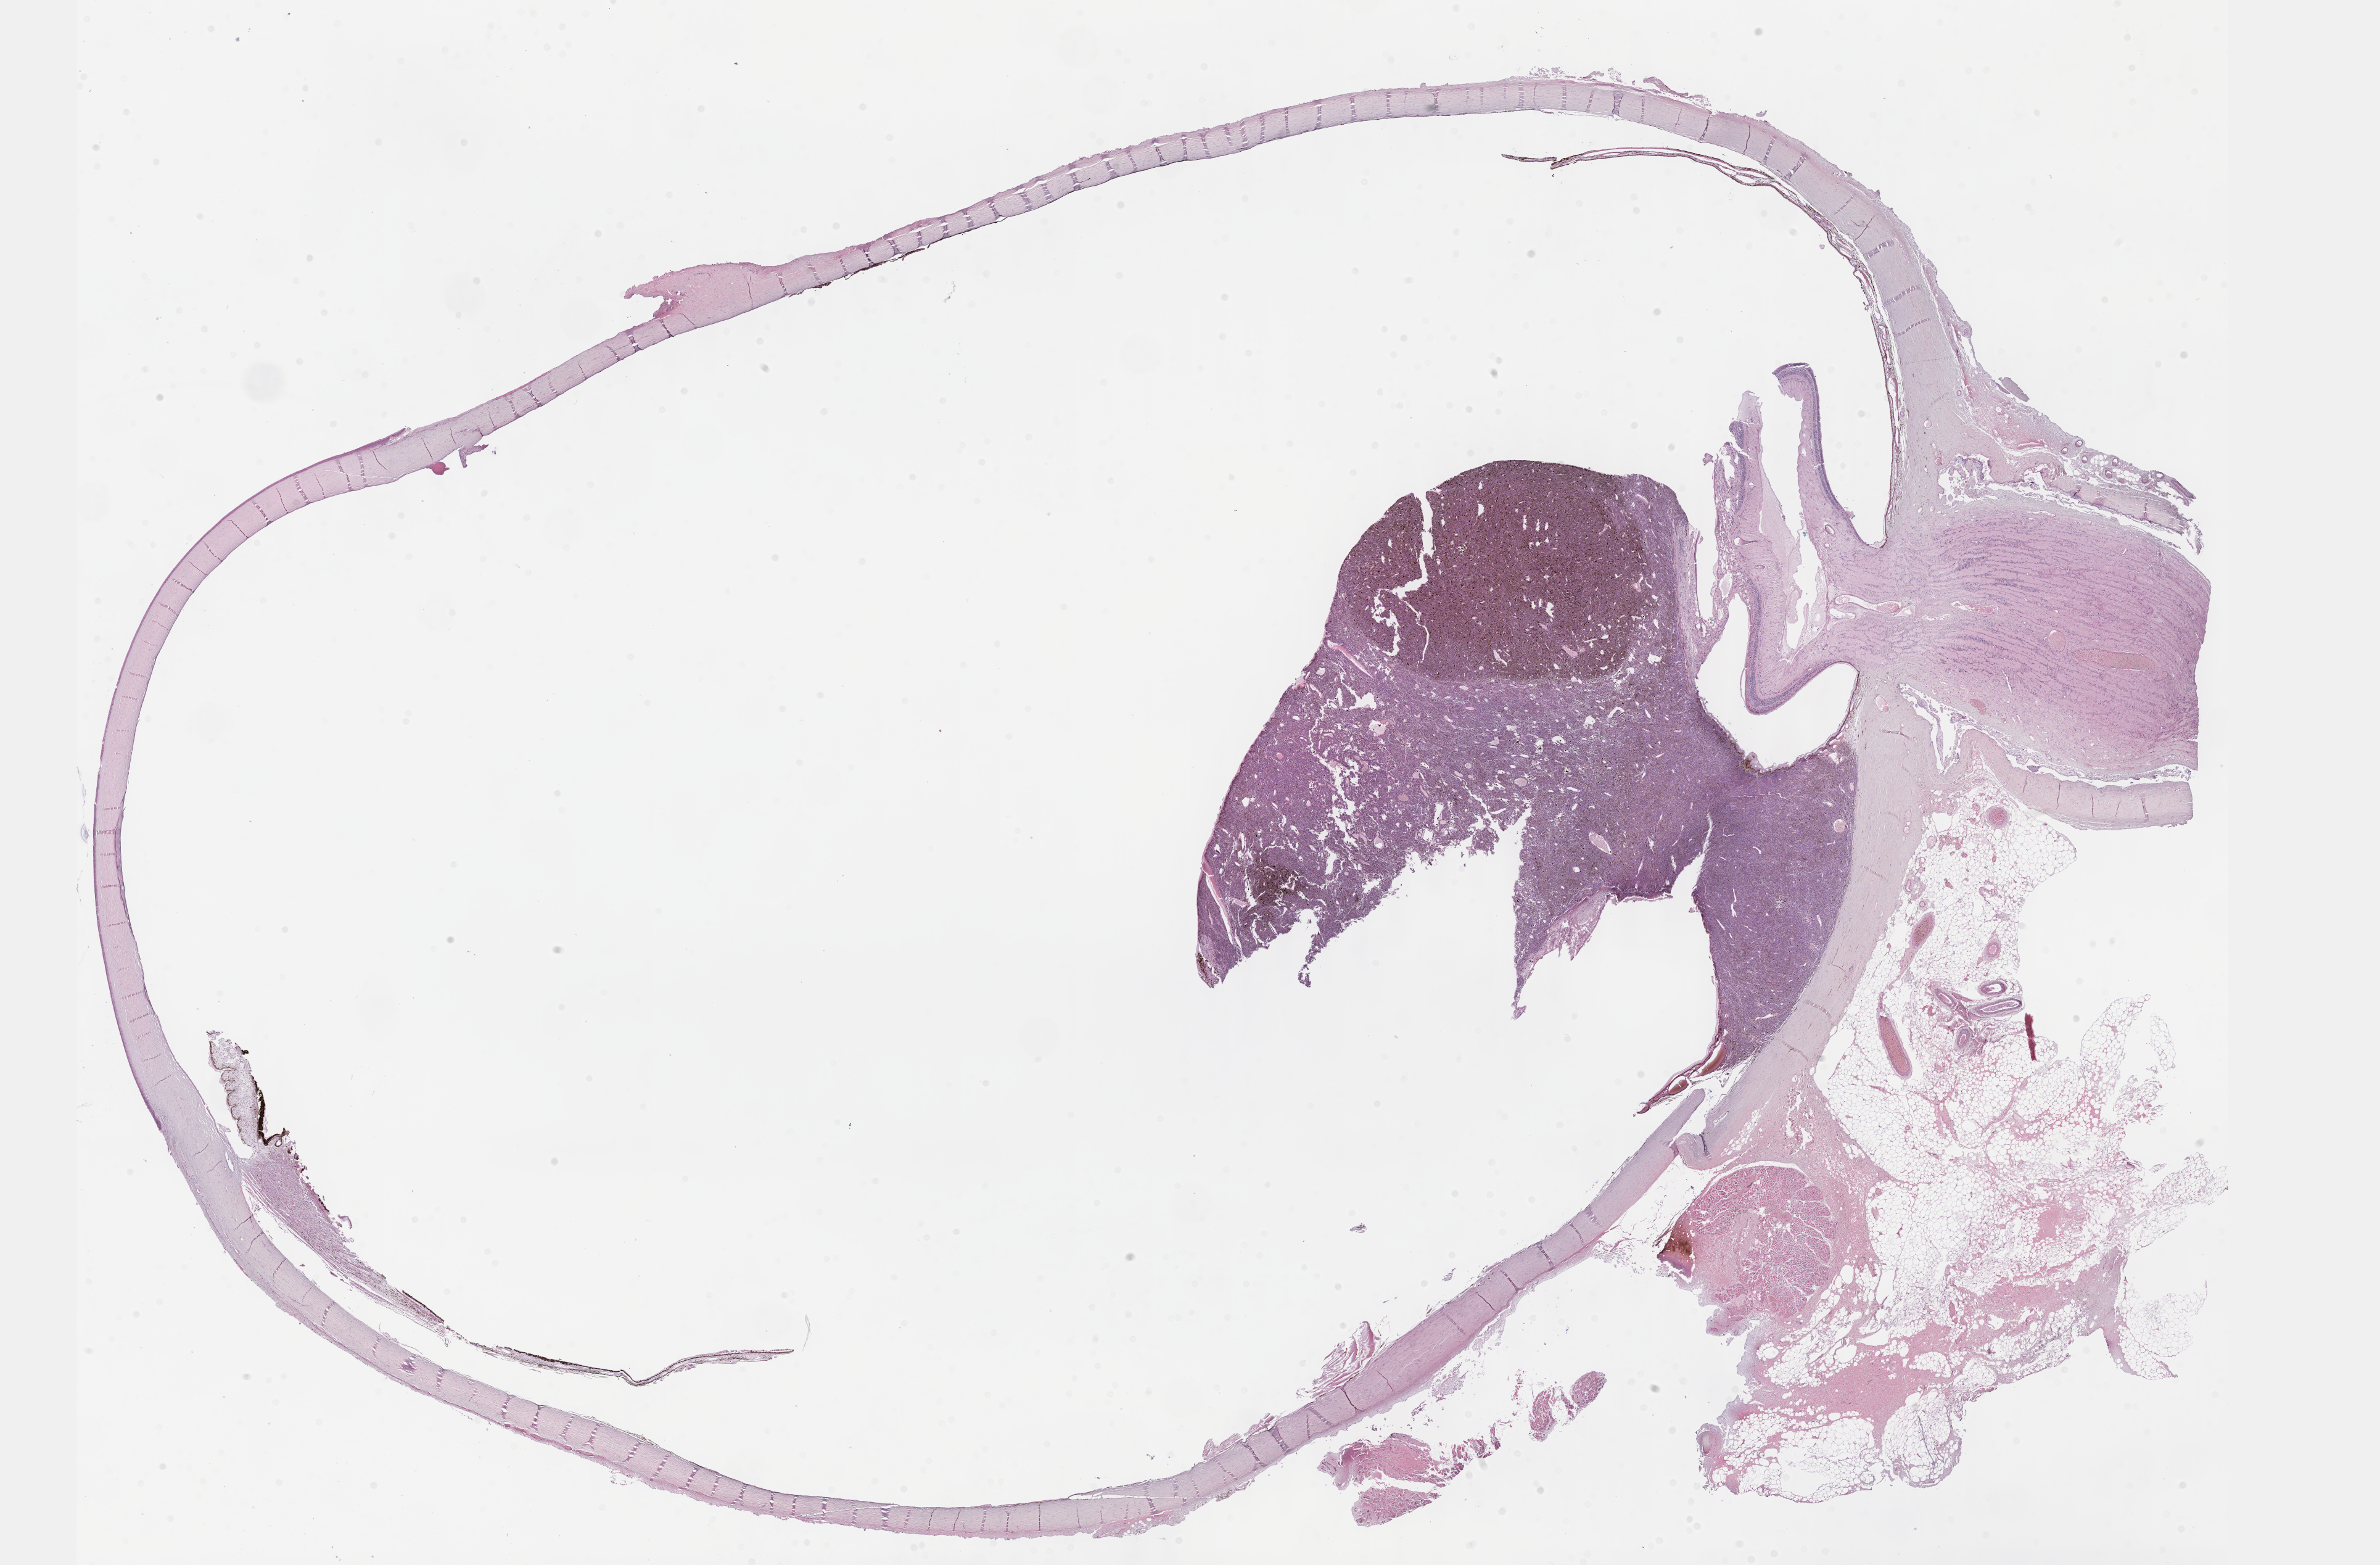
H&E whole-slide image, shown as a low-resolution overview of the whole scanned area (about 31.2 x 20.5 mm). Formalin-fixed paraffin-embedded (FFPE) diagnostic section. Primary tumour sample from the uvea. Patient: male, age at initial diagnosis 38 years.
- histologic diagnosis: Spindle cell melanoma, NOS (choroid)
- AJCC pathologic stage: IIB